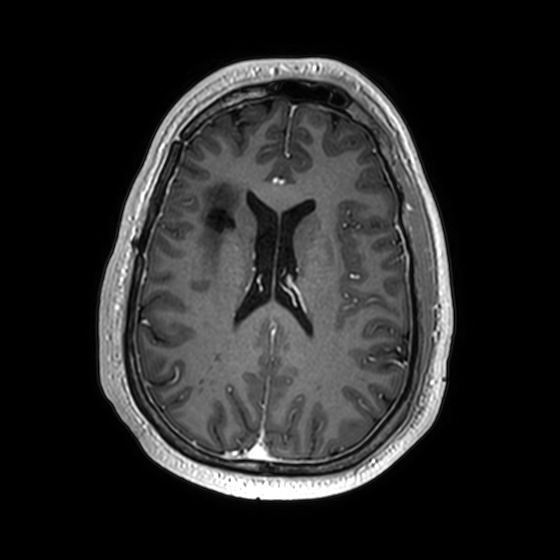
Brain MRI from a brain-tumour surgery series, one axial slice; slice 73 of 174 in the series (ordered by position); T1-weighted post-contrast; 1 mm slice thickness; 560 × 560 image matrix, field of view 256 × 256 mm. From the clinical record (not read from this slice): histopathology: Astrocytoma; WHO grade: 2; IDH mutation: yes; tumour location: Right Insular.
Annotated regions visible in this slice (expert manual segmentation):
- previous resection cavity: bounding box [x1, y1, x2, y2] px = [207, 207, 233, 231]